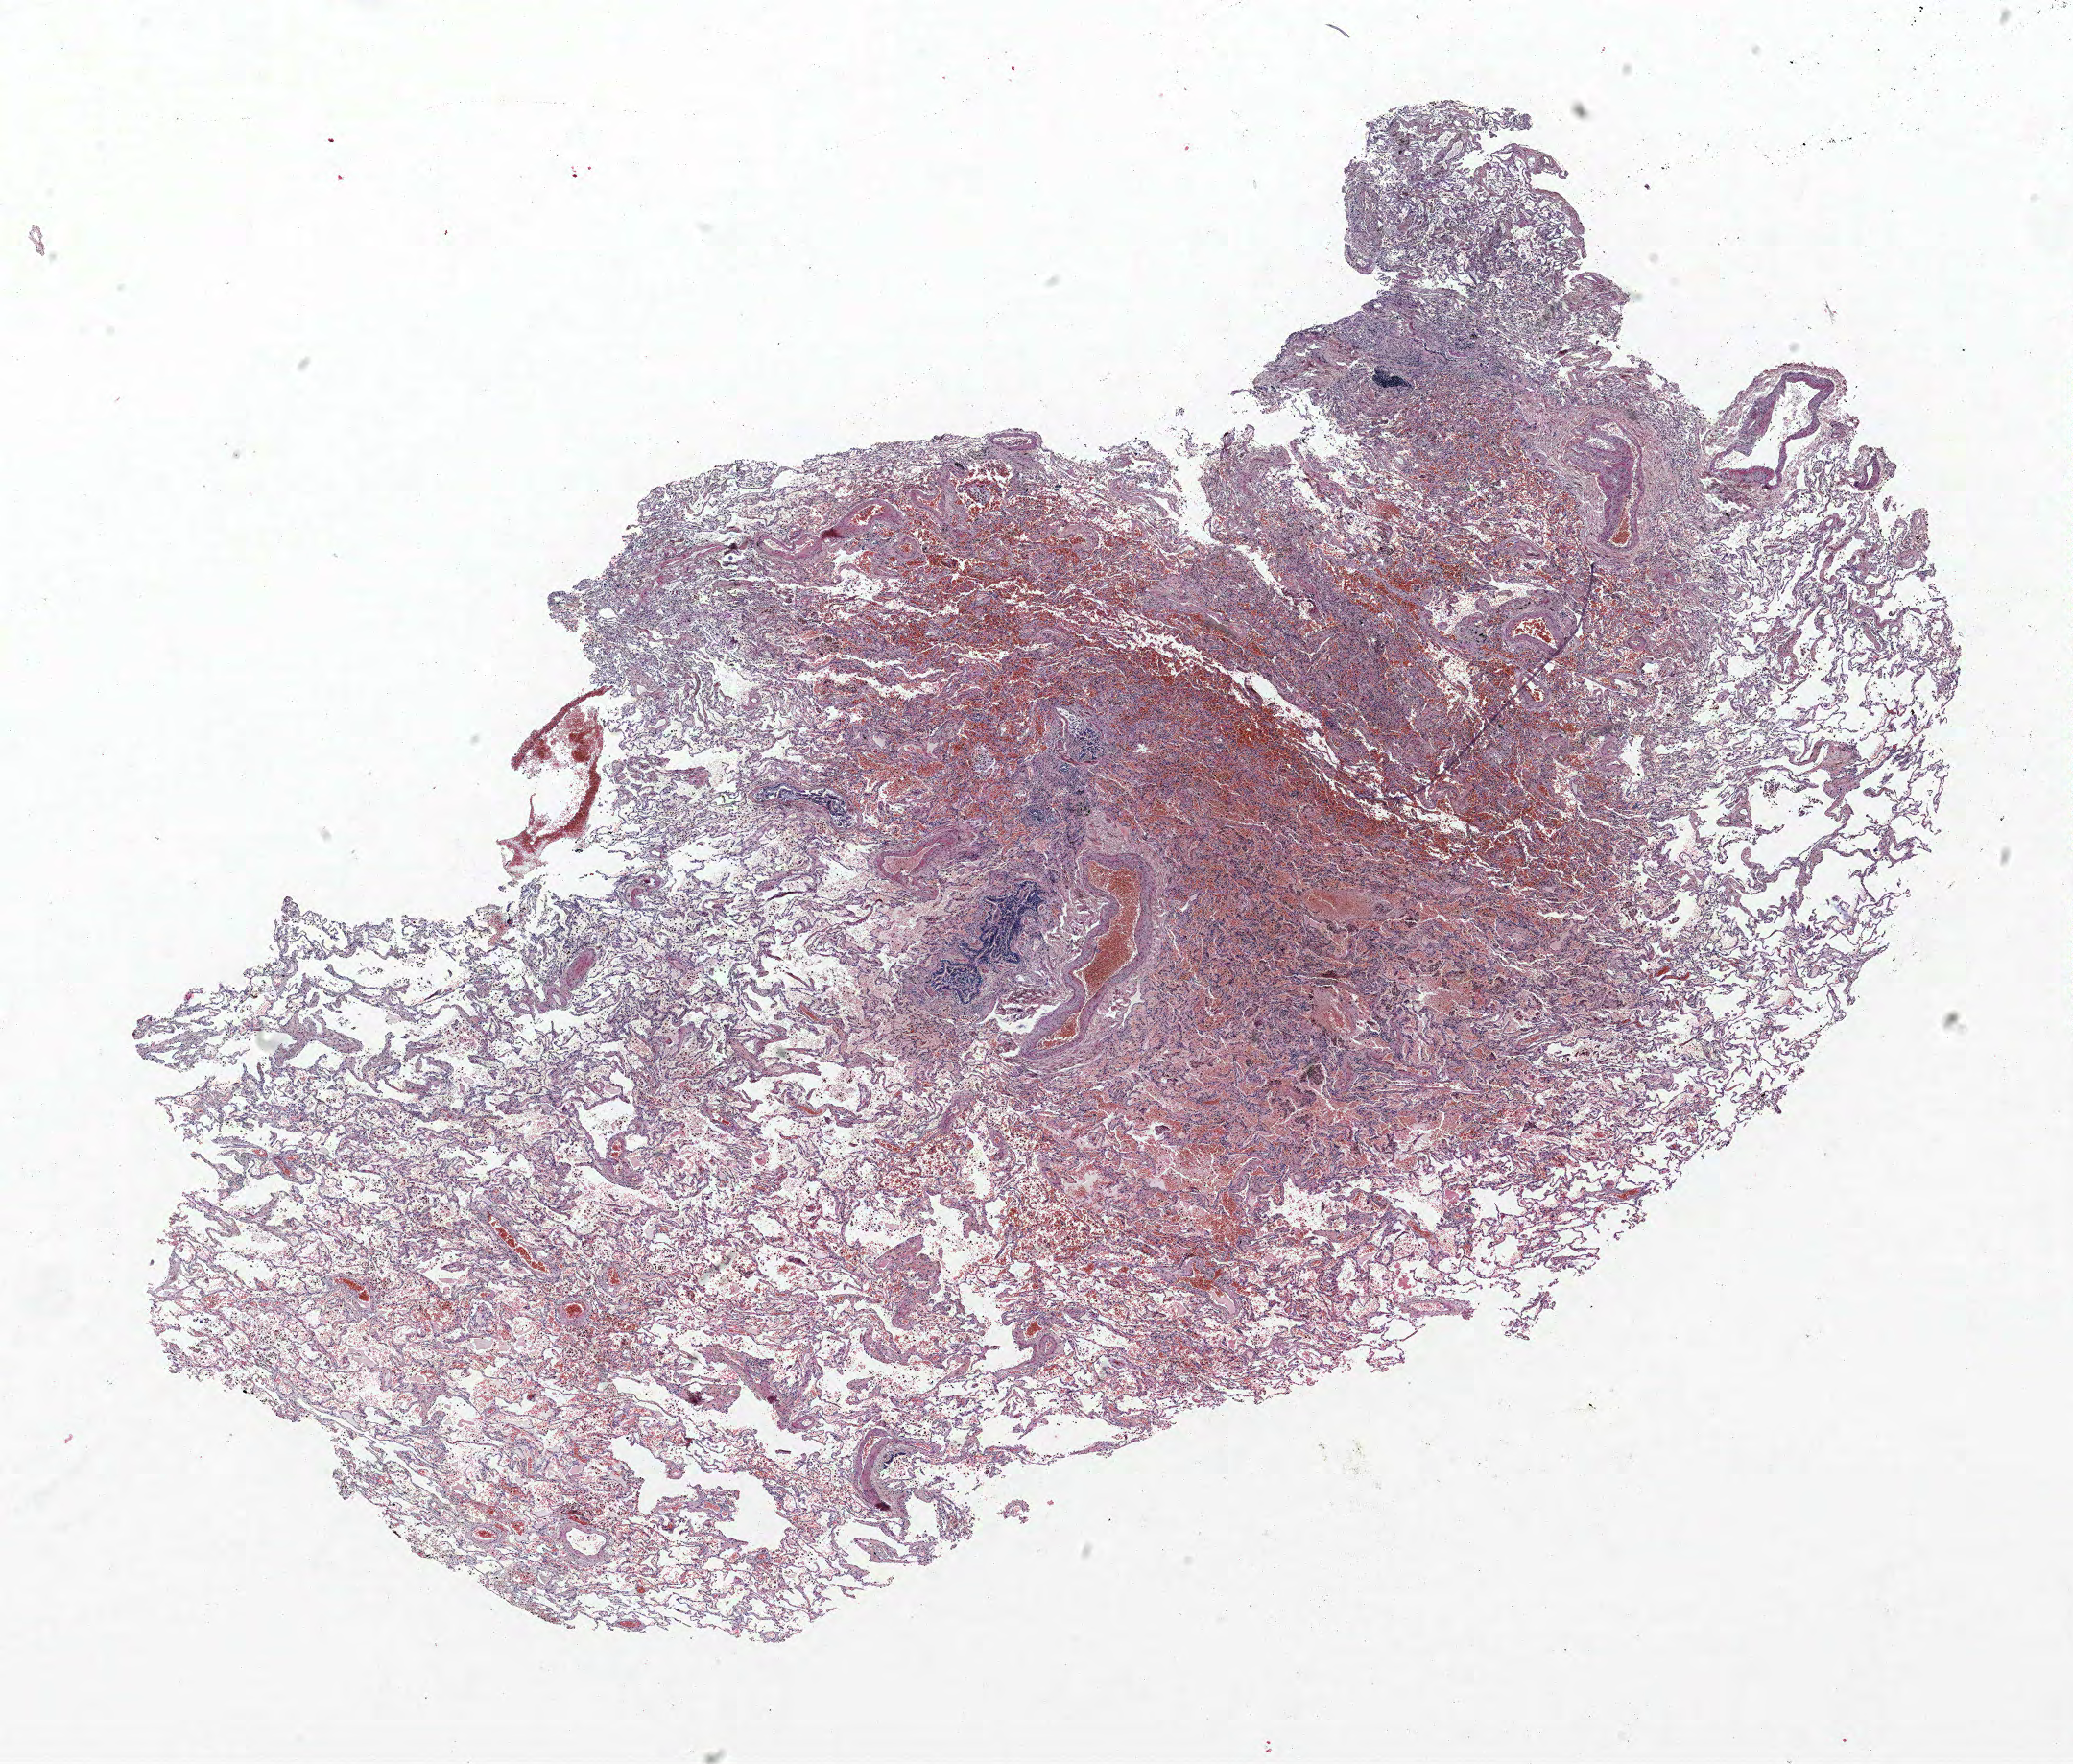
Whole-slide histology image, Hematoxylin and eosin (H&E) stained, a low-resolution overview of the entire scanned area, about 17.3 x 14.7 mm (slide scanned at 40x); FFPE section; lung. Male patient, aged 64 at enrolment. Grade: poorly differentiated (G3).
Participant's lung-cancer diagnosis: Neuroendocrine carcinoma, NOS. Stage (AJCC 6th edition): IIIA. ICD-O-3 topography: upper lobe of lung (C34.1). Tumour size (pathology): 11 mm. Primary tumour location (clinical record): left upper lobe.